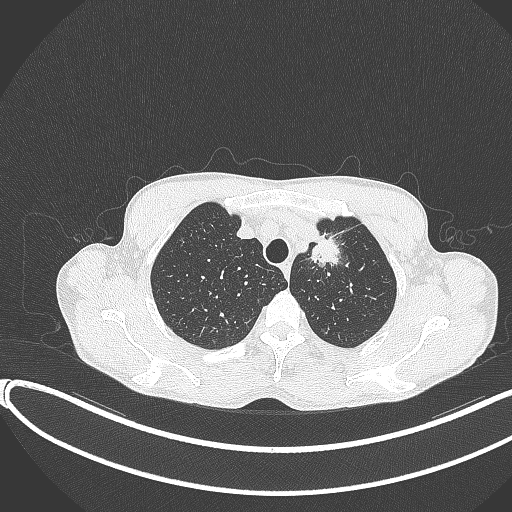
Chest CT, one axial slice. Position 321 of 374 along the scan axis. Lung window (W 1500 / L -600 HU). 512 × 512 image matrix, field of view 400 × 400 mm. Male patient, age 58 years. From the clinical record (not read from this slice): clinical TNM (as recorded): T1c N1 M0.
Structures marked on this image (rectangle marked by the reading radiologist):
- lung tumour (recorded histology: adenocarcinoma): bounding box [x1, y1, x2, y2] px = [306, 227, 351, 271]